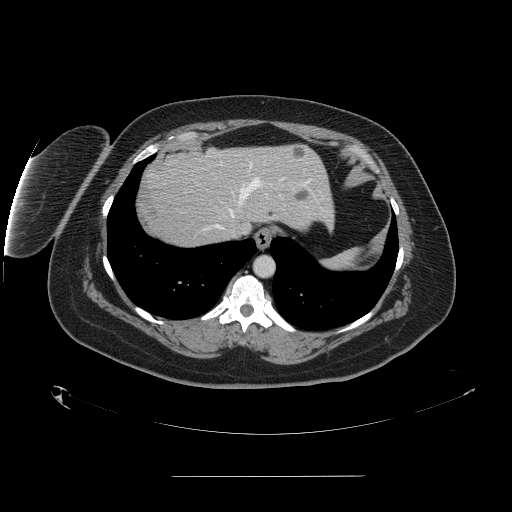
Contrast-enhanced abdominal CT, one axial slice; slice 132 of 164 in the series (ordered by position); intravenous contrast given; soft-tissue window (W 400 / L 40 HU); 512 × 512 image matrix, field of view 495 × 495 mm. Female patient, age 52 years. Case-level facts recorded for this patient, not image findings: diagnosis: colorectal cancer liver metastases, imaged before liver resection; multiple liver metastases: yes; largest metastasis: 3.5 cm; chemotherapy before resection: no.
Structures marked on this image (expert manual segmentation):
- hepatic veins: bounding box (x1, y1, x2, y2) in pixels: (215, 164, 284, 237)
- liver: (144, 145, 333, 247)
- planned liver remnant (the part of the liver to remain after resection): (174, 145, 334, 229)
- liver metastasis: (297, 192, 308, 201)
- liver metastasis: (265, 209, 274, 217)
- liver metastasis: (294, 149, 306, 157)